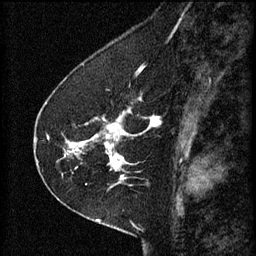
Breast MRI (dynamic contrast-enhanced), one sagittal slice. Slice 23 of 60 in the series (ordered by position). 3 images stored at this slice position (order not interpretable as contrast timing). 1.5 T. TE 4.2 ms, TR 8.2 ms. 2 mm slice thickness. 256 × 256 image matrix. Patient: female, 41 years.
Annotated regions visible in this slice (semi-automatic segmentation, software-assisted and operator-edited):
- analysis volume of interest (the breast-tissue region the enhancement analysis was run in; not a lesion): box from (x=68, y=92) to (x=158, y=173) px
- tumour enhancement mask (voxels above the 70 % enhancement threshold inside the analysis volume of interest): (x=68, y=112)–(x=157, y=171)